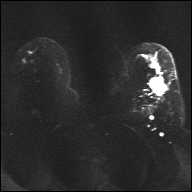
Breast MRI, one axial slice; position 22 of 32 along the scan axis; diffusion-weighted series; image 2 of 4 stored at this slice position (different b-values; order by instance number); 1.5 T; 192 × 192 image matrix. Female patient.
Structures marked on this image (manually delineated by an expert):
- tumour on diffusion-weighted imaging: bounding box <150,77,166,95> (left, top, right, bottom; pixels)